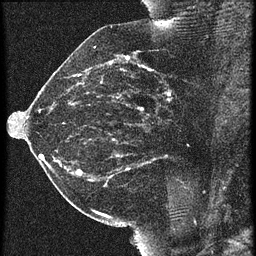
Breast MRI (dynamic contrast-enhanced), one sagittal slice. Position 25 of 60 along the scan axis. 3 images stored at this slice position (order not interpretable as contrast timing). 1.5 T. TE 4.2 ms, TR 21.3 ms. 256 × 256 image matrix. Female patient, age 42 years. Case-level facts recorded for this patient, not image findings: setting: breast cancer imaged before/during neoadjuvant chemotherapy; receptor status: HER2-positive.
Structures marked on this image (semi-automatically segmented with operator editing):
- analysis volume of interest (the breast-tissue region the enhancement analysis was run in; not a lesion): bounding box [x1, y1, x2, y2] px = [122, 82, 195, 147]
- tumour enhancement mask (voxels above the 90 % enhancement threshold inside the analysis volume of interest): [141, 84, 170, 109]